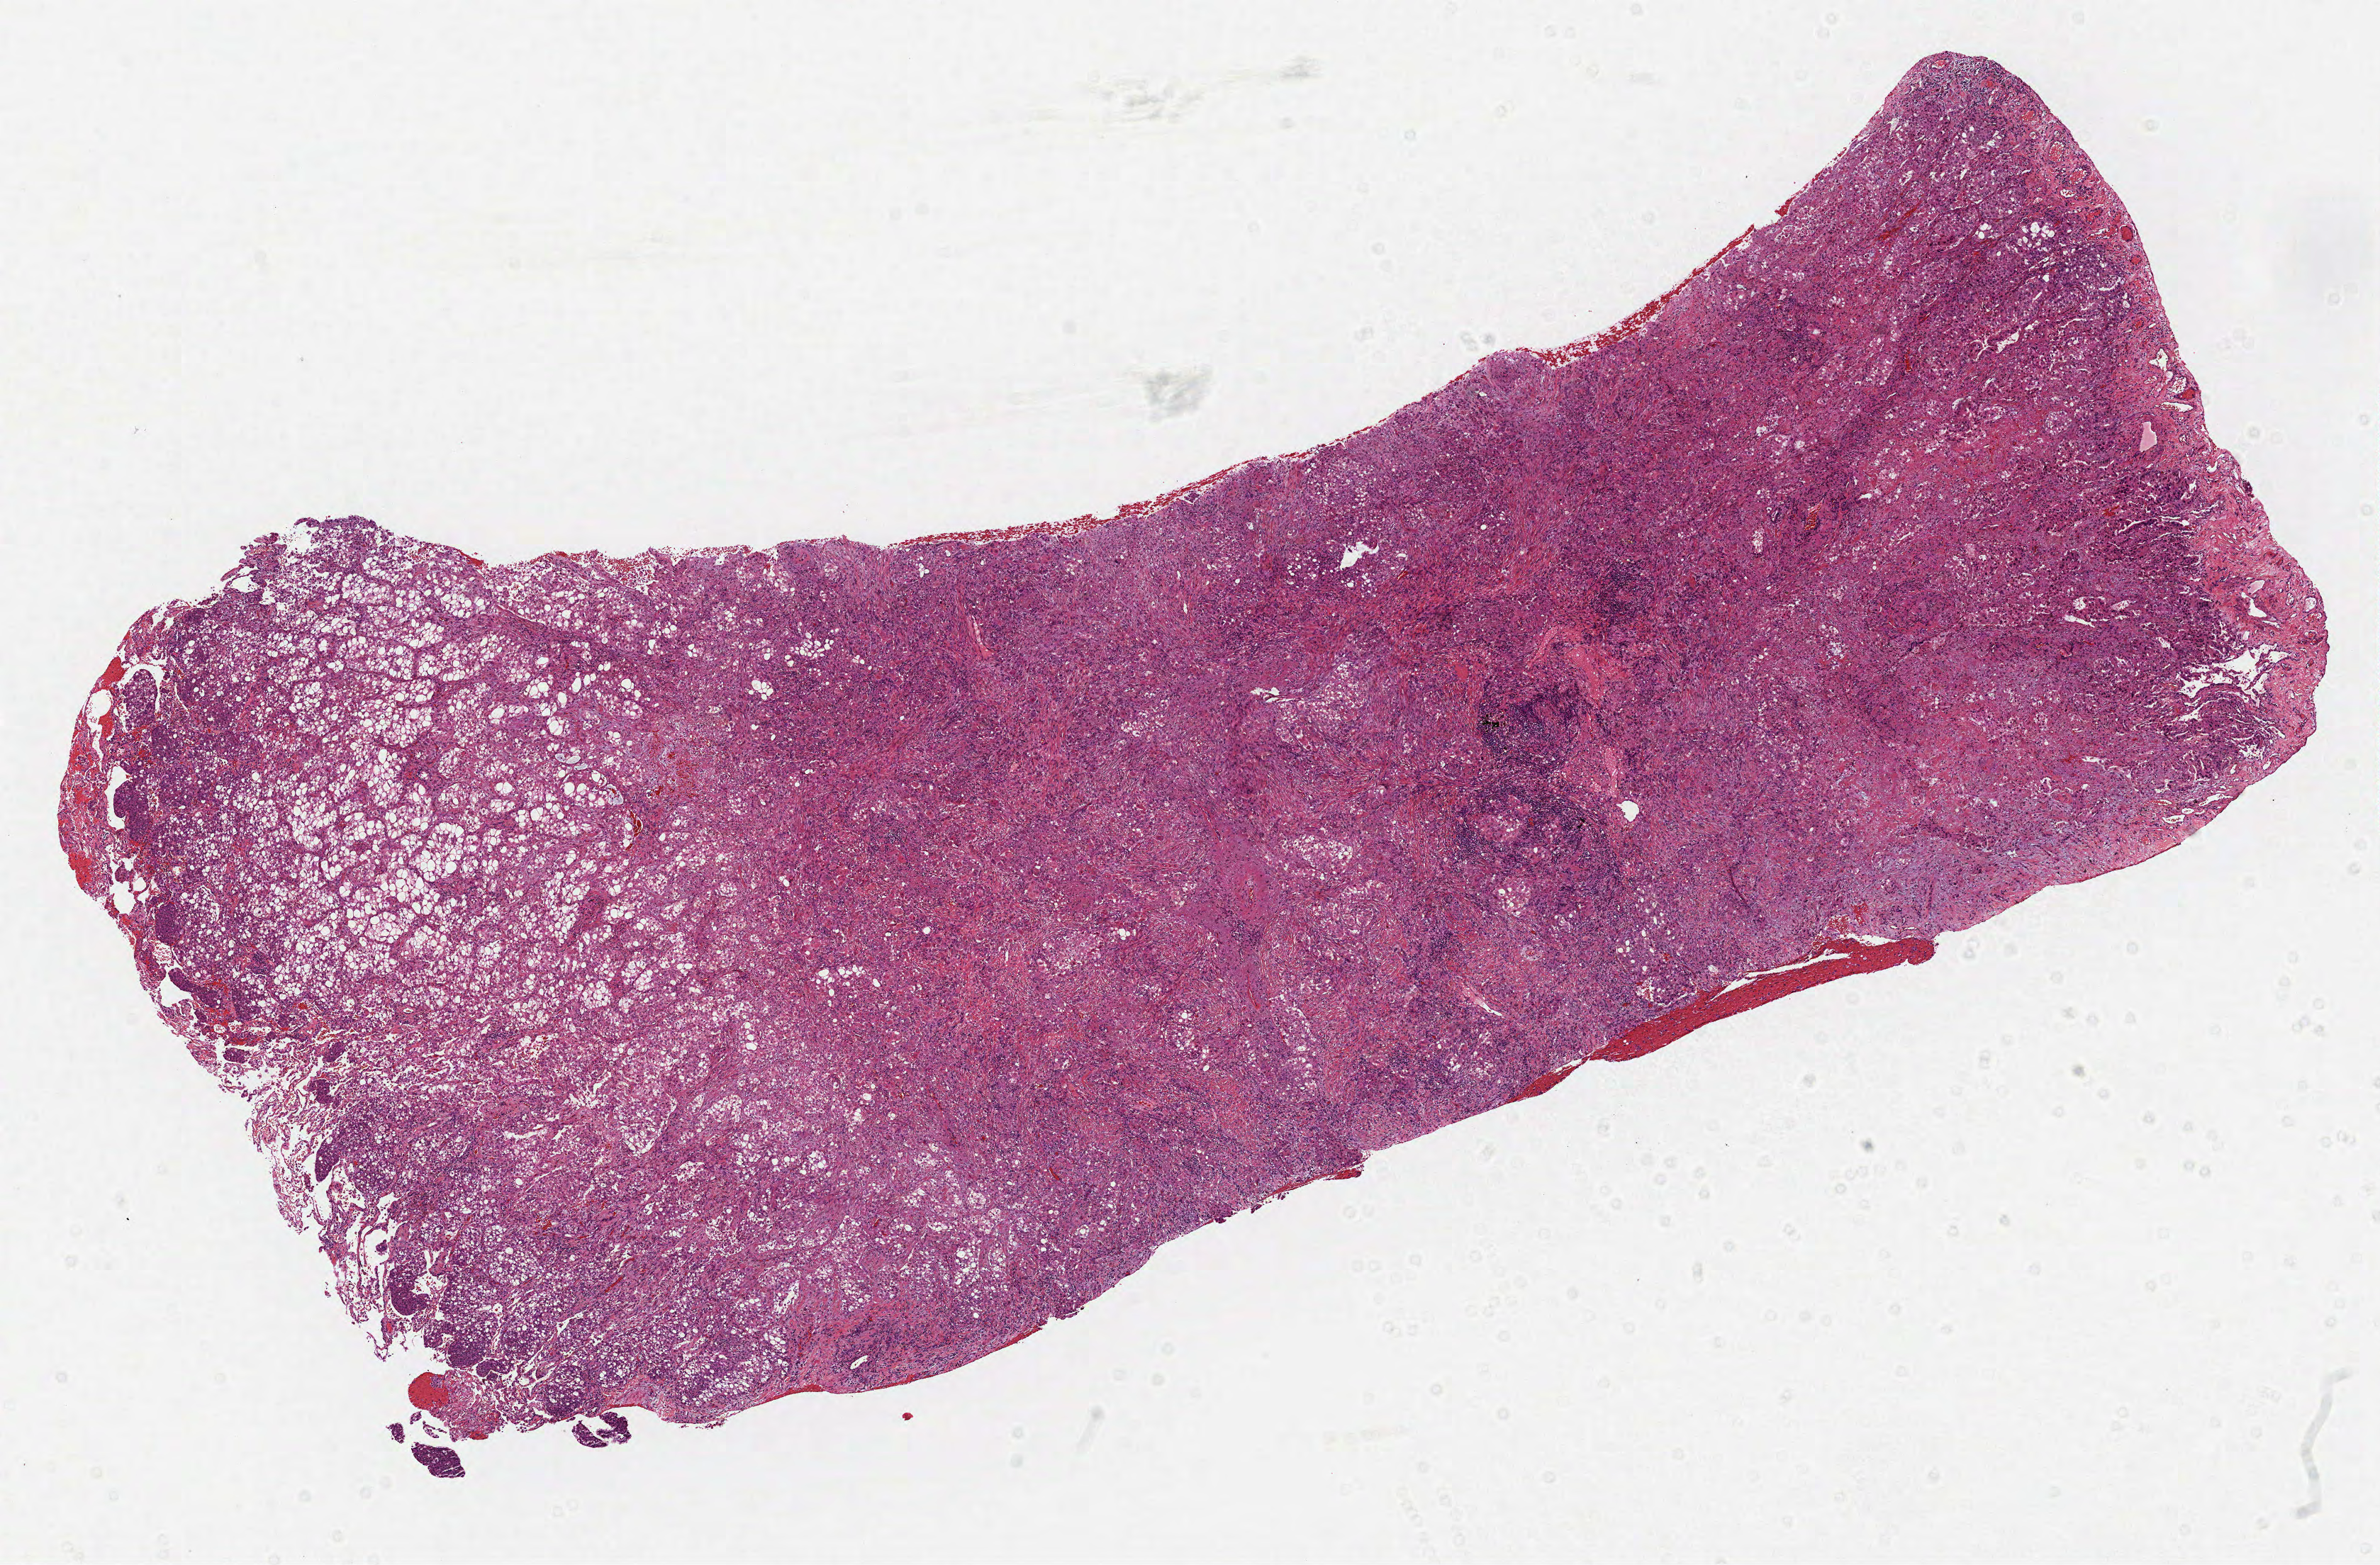
H&E whole-slide image, shown as a low-resolution overview of the whole scanned area (about 13.5 x 8.9 mm); formalin-fixed paraffin-embedded (FFPE) diagnostic section; lung, primary tumour sample. Female patient; age at initial diagnosis 77 years.
TNM: T1b N0 M0. AJCC pathologic stage: IA (6th edition). Pathologic diagnosis: Adenocarcinoma, NOS (lower lobe, lung).